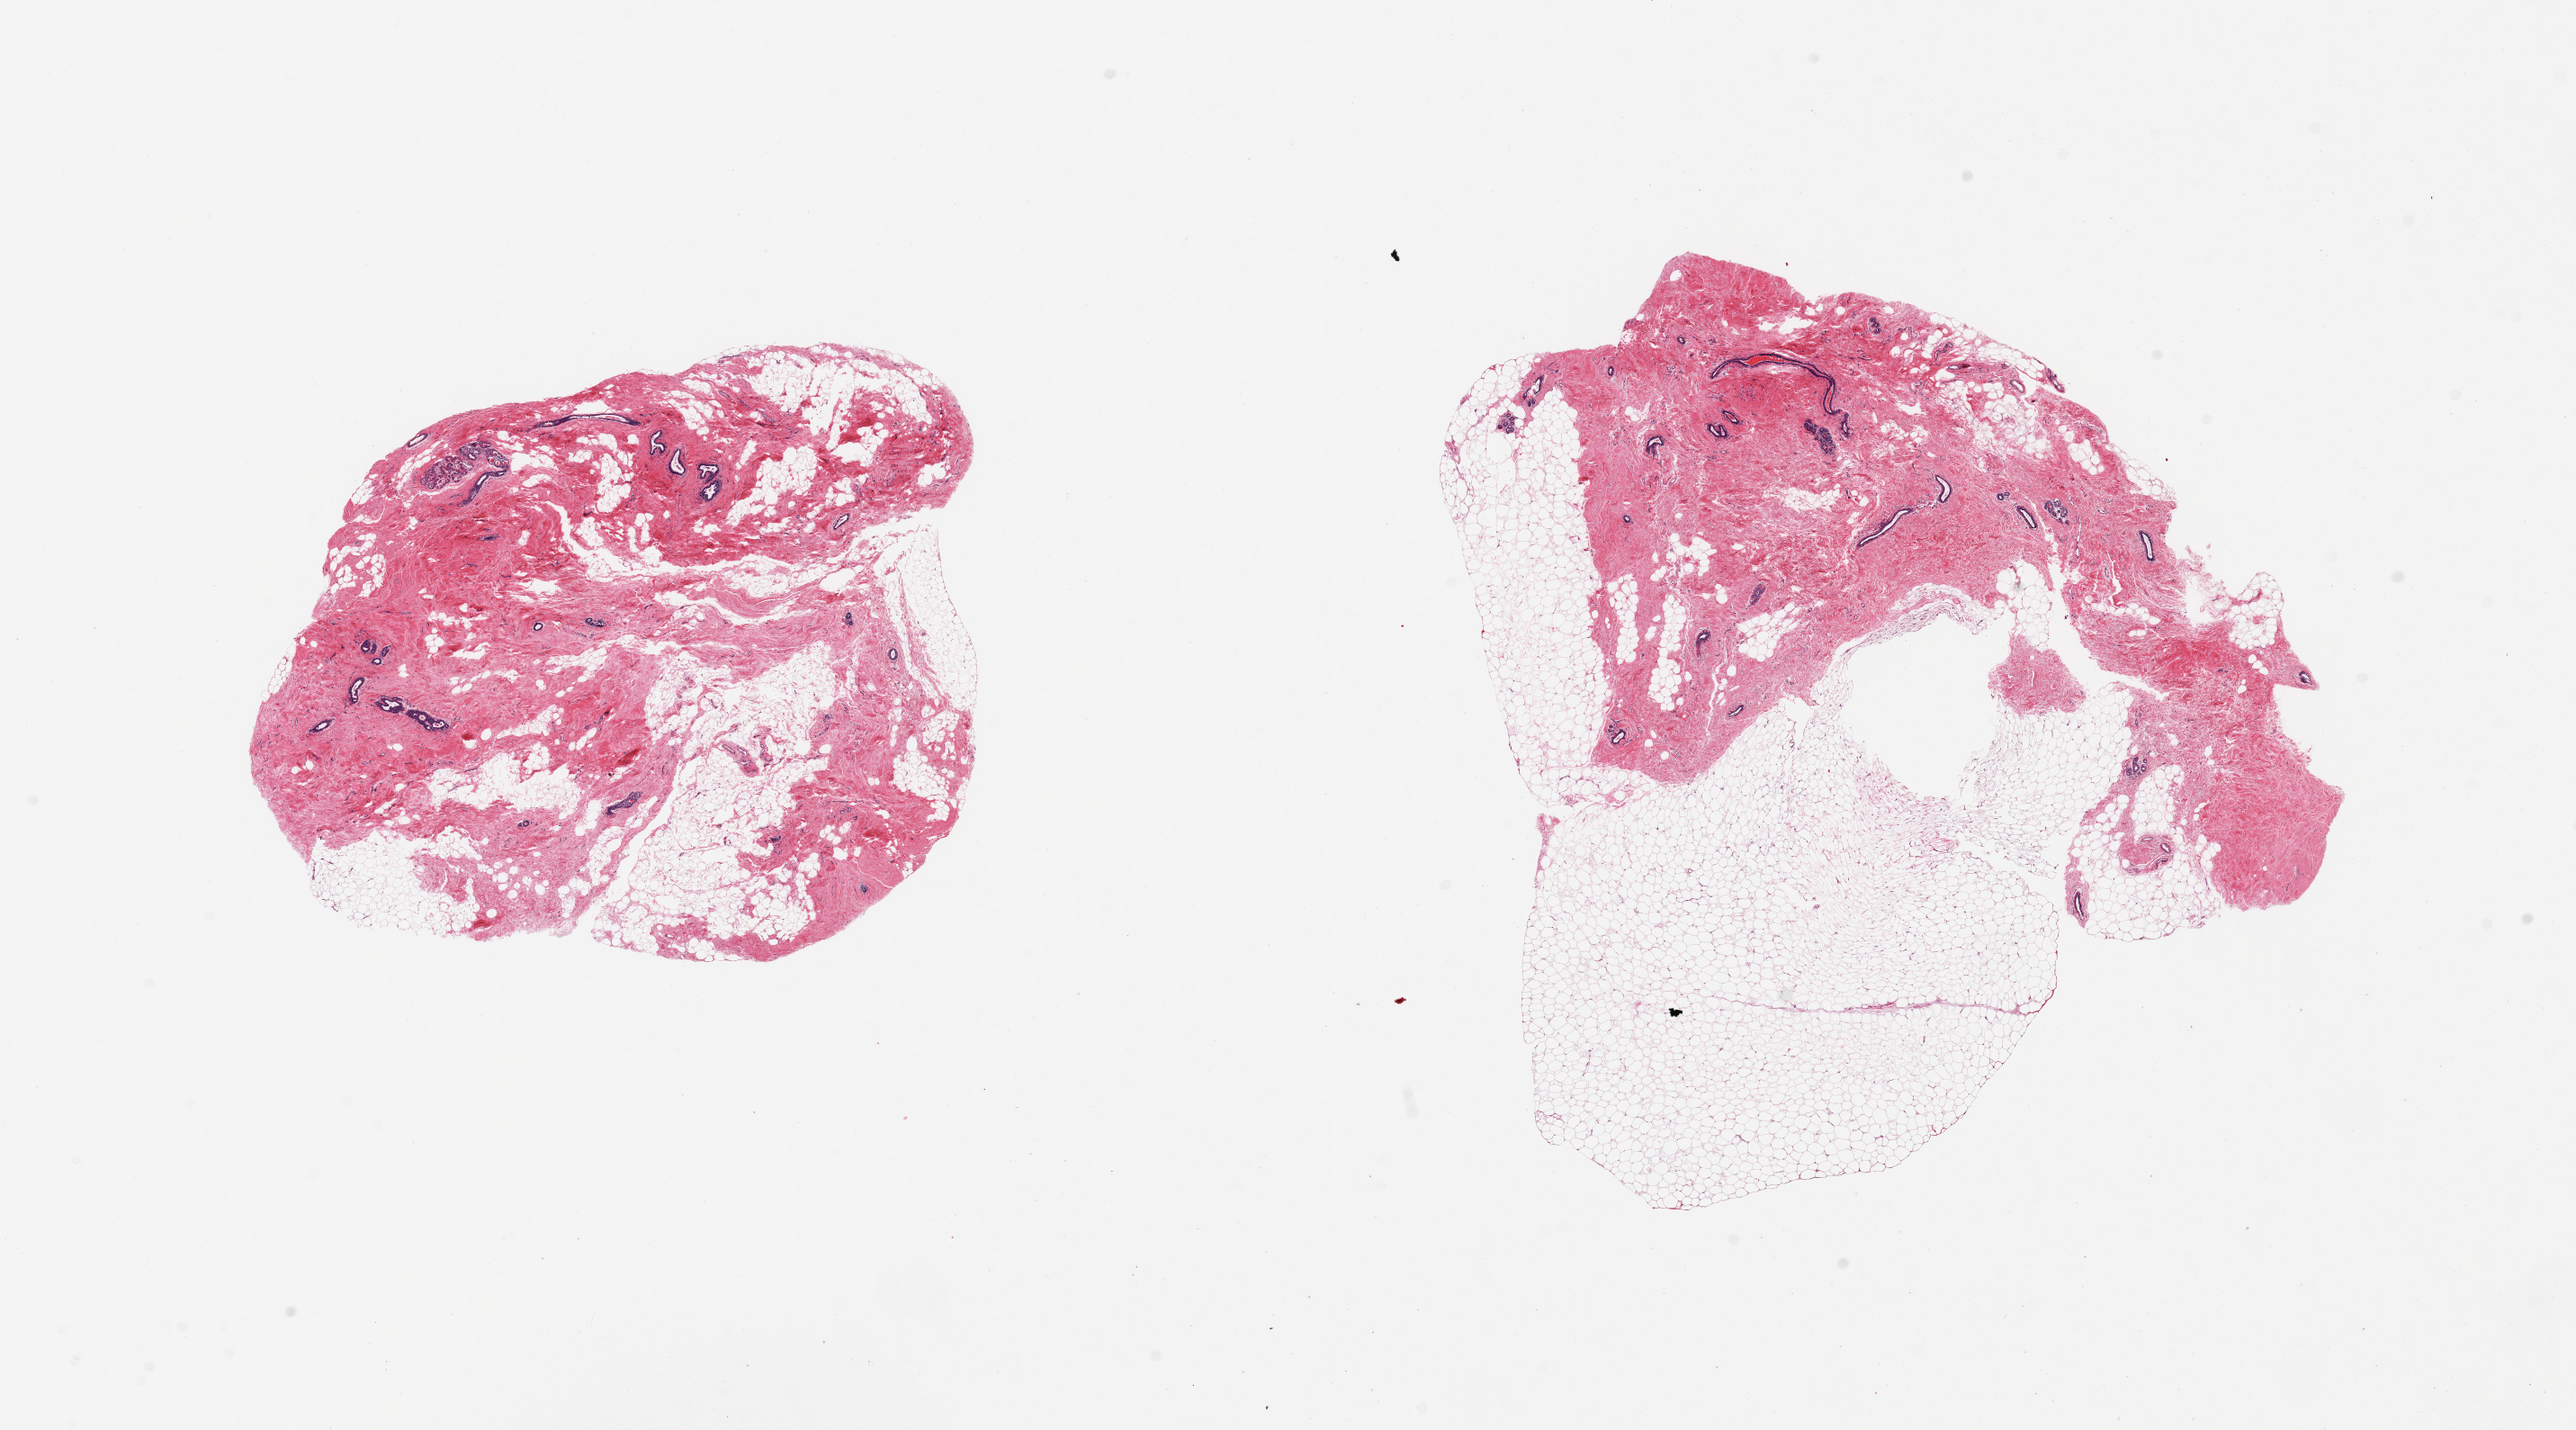
Whole-slide image, hematoxylin and eosin (H&E) stain — whole scanned area (about 22.6 x 12.6 mm) shown as a low-resolution overview; PAXgene-fixed, paraffin-embedded tissue; sampled site (target tissue): breast; tissue donor sample. Female donor.
Pathologist's review note for this sample: 2 pieces; dense fibrofatty stroma and scattered ductal structures with a few residual small atrophic lobules, 30 and 50% fat.